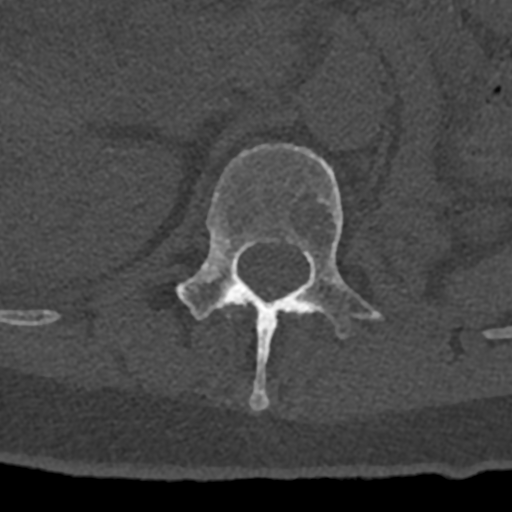
CT including the spine, one axial slice; slice 443 of 797 in the series (ordered by position); reconstruction kernel Br40s/3; 120 kVp; bone window (W 1800 / L 400 HU); 0.5 mm slice thickness; 512 × 512 image matrix, field of view 160 × 160 mm. Patient: male, 74 years. From the clinical record (not read from this slice): primary cancer: renal.
Annotated regions visible in this slice (semi-automatically segmented with operator editing):
- L1 vertebra: box from (x=175, y=143) to (x=382, y=411) px
- T12 vertebra: (x=224, y=301)–(x=246, y=307)